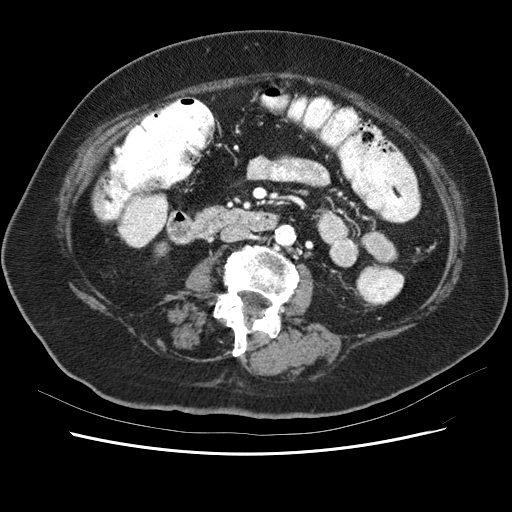
Contrast-enhanced abdominal CT (liver protocol), one axial slice; slice 7 of 62 in the series (ordered by position); 120 kVp; soft-tissue window (W 400 / L 40 HU); 2.5 mm slice thickness; 512 × 512 image matrix, field of view 340 × 340 mm. From the clinical record (not read from this slice): diagnosis: hepatocellular carcinoma (patient treated with transarterial chemoembolisation; whether this scan precedes or follows treatment is not stated here); TNM stage (as recorded): Stage-I; Child-Pugh class: B; tumour nodularity: uninodular; tumour size: 5.3 cm.
Outlined on this slice (semi-automatic segmentation, software-assisted and operator-edited):
- liver parenchyma outside the tumour (the mass and vessels are separate outlines, so this box may not span the whole liver): bounding box [x1, y1, x2, y2] px = [129, 198, 136, 202]